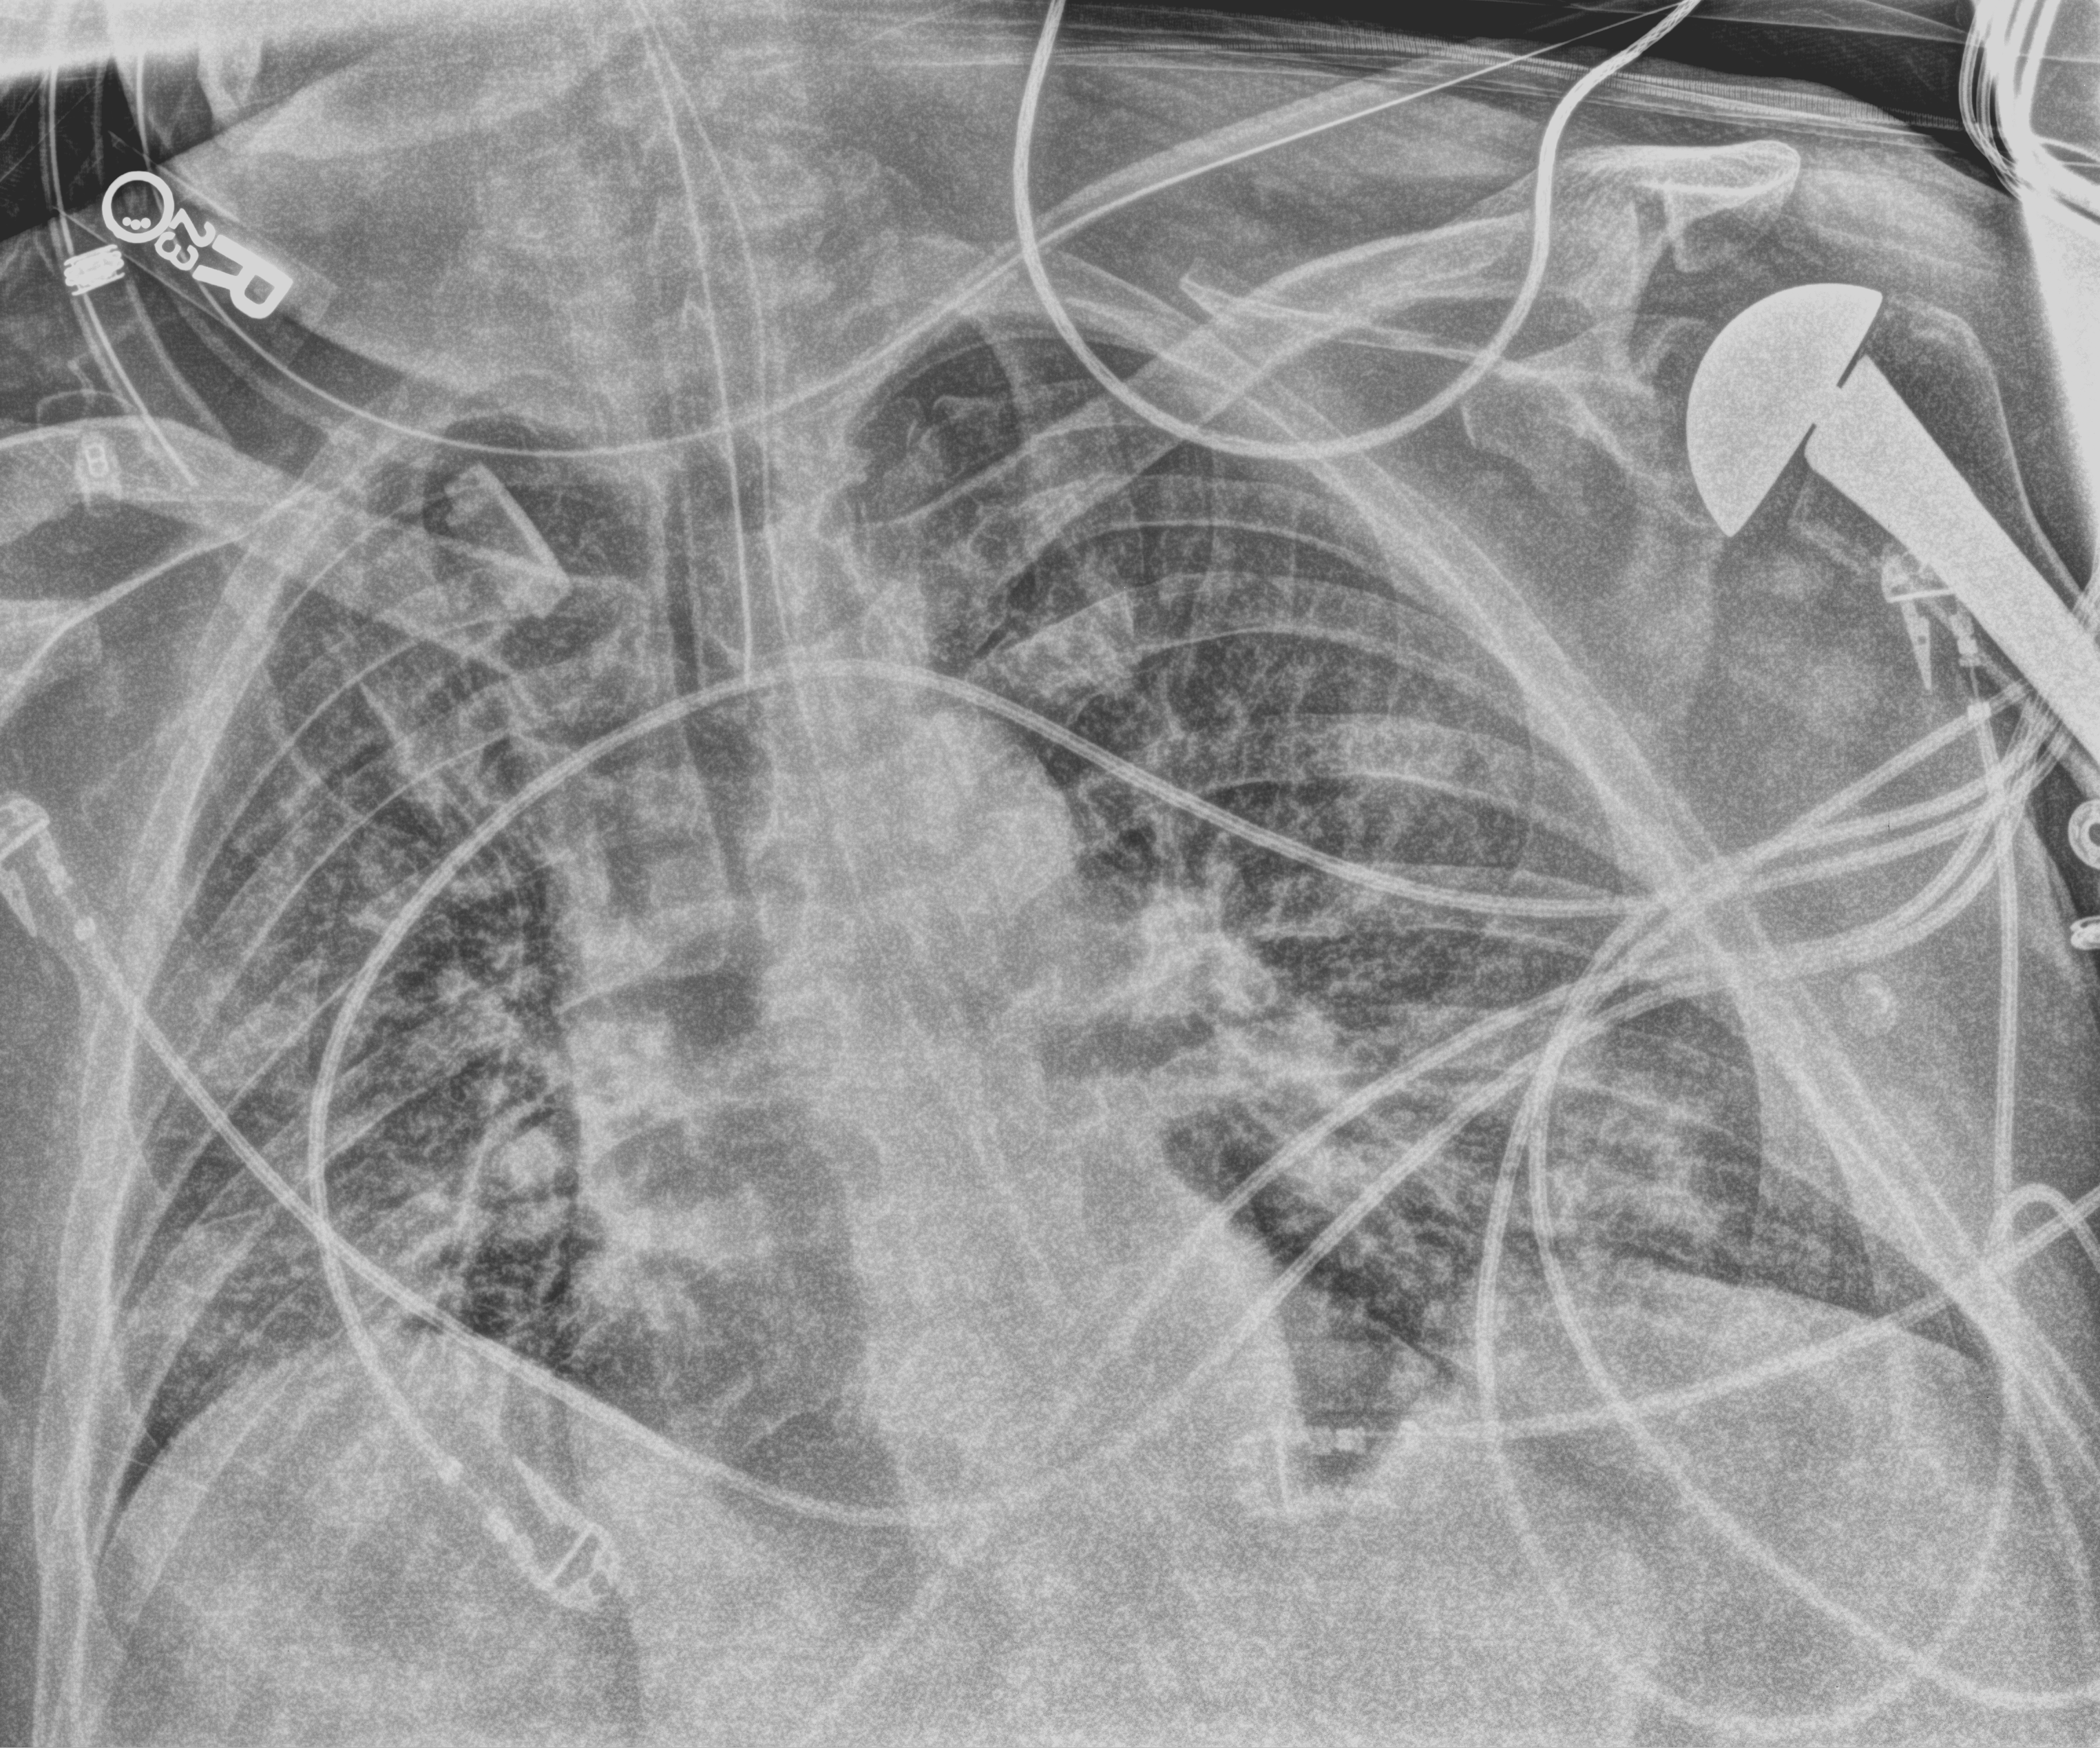
Chest X-ray (portable), anteroposterior (AP) projection. Male patient hospitalised with COVID-19, age 60–74 years.
Hospital-stay facts (about this admission, not read from this image; timing relative to this image not recorded):
- admitted to intensive care during this hospital stay: yes
- smoking status (admission record): former